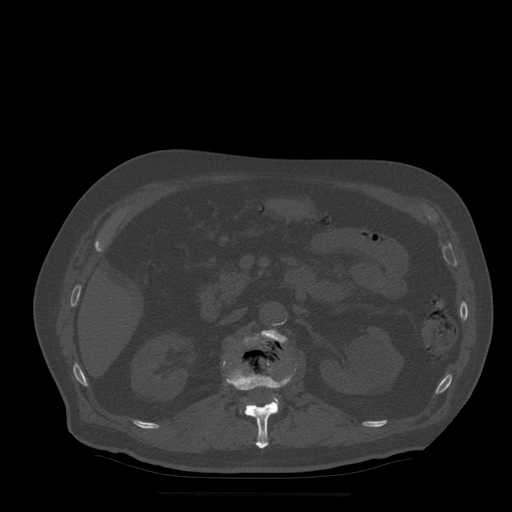
CT including the spine, one axial slice. Position 187 of 522 along the scan axis. Bone window (W 1800 / L 400 HU). 1.25 mm slice thickness. 512 × 512 image matrix, field of view 420 × 420 mm. Patient age 72 years. Case-level facts recorded for this patient, not image findings: primary cancer: prostate.
Annotated regions visible in this slice (semi-automatic segmentation, software-assisted and operator-edited):
- L1 vertebra: bounding box [x1, y1, x2, y2] px = [227, 362, 297, 449]
- L2 vertebra: [244, 329, 287, 414]